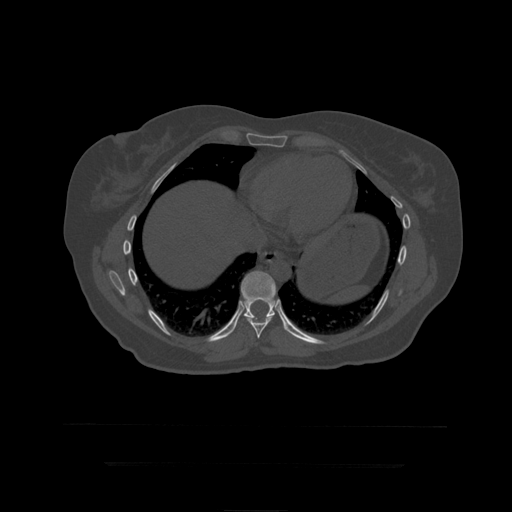
CT including the spine, one axial slice; slice 252 of 399 in the series (ordered by position); reconstruction kernel STANDARD; 120 kVp; bone window (W 1800 / L 400 HU); 1.25 mm slice thickness; 512 × 512 image matrix, field of view 450 × 450 mm. Patient age 41 years. Case-level facts recorded for this patient, not image findings: primary cancer: breast.
Annotated regions visible in this slice (semi-automatically segmented with operator editing):
- T10 vertebra: bounding box <241,271,277,320> (left, top, right, bottom; pixels)
- T9 vertebra: <247,316,273,339>